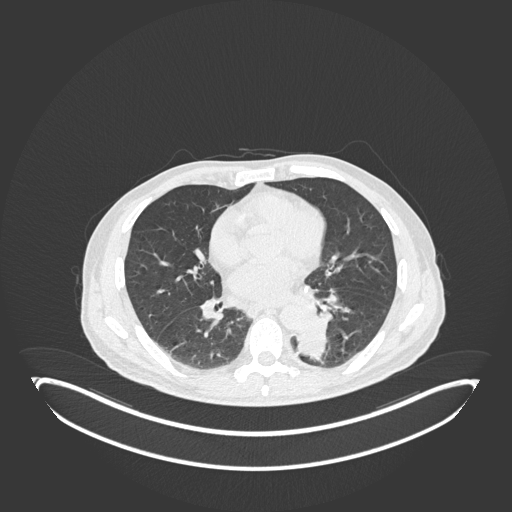
Chest CT, one axial slice. Position 84 of 251 along the scan axis. Lung window (W 1500 / L -600 HU). 1 mm slice thickness. 512 × 512 image matrix, field of view 500 × 500 mm. Patient: male, 72 years. Case-level facts recorded for this patient, not image findings: clinical TNM (as recorded): T2b N0 M1.
Annotated regions visible in this slice (rectangle marked by the reading radiologist):
- lung tumour (recorded histology: adenocarcinoma): bounding box (x1, y1, x2, y2) in pixels: (287, 310, 333, 364)